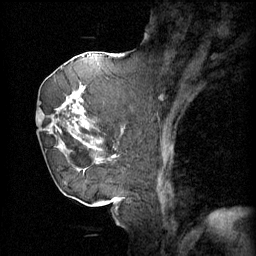
Breast MRI (dynamic contrast-enhanced), one sagittal slice; position 24 of 60 along the scan axis; 4 images stored at this slice position (order not interpretable as contrast timing); 1.5 T; TE 4.2 ms, TR 11 ms; 2 mm slice thickness; 256 × 256 image matrix, field of view 220 × 220 mm. Patient: female, 72 years.
Outlined on this slice (semi-automatic segmentation, software-assisted and operator-edited):
- analysis volume of interest (the breast-tissue region the enhancement analysis was run in; not a lesion): bounding box (x1, y1, x2, y2) in pixels: (44, 68, 109, 163)
- tumour enhancement mask (voxels above the 70 % enhancement threshold inside the analysis volume of interest): (44, 82, 108, 159)